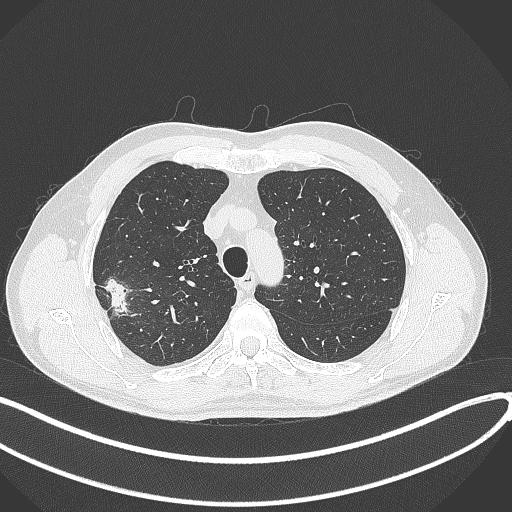
Chest CT, one axial slice. Position 321 of 381 along the scan axis. Reconstruction kernel B70f. 120 kVp. Lung window (W 1500 / L -600 HU). 1 mm slice thickness. 512 × 512 image matrix, field of view 400 × 400 mm. Male patient, age 62 years. Case-level facts recorded for this patient, not image findings: clinical TNM (as recorded): T1c N0 M0; histopathological grade: G2-3.
Structures marked on this image (bounding box drawn by a radiologist):
- lung tumour (recorded histology: adenocarcinoma): bounding box (x1, y1, x2, y2) in pixels: (104, 275, 132, 319)